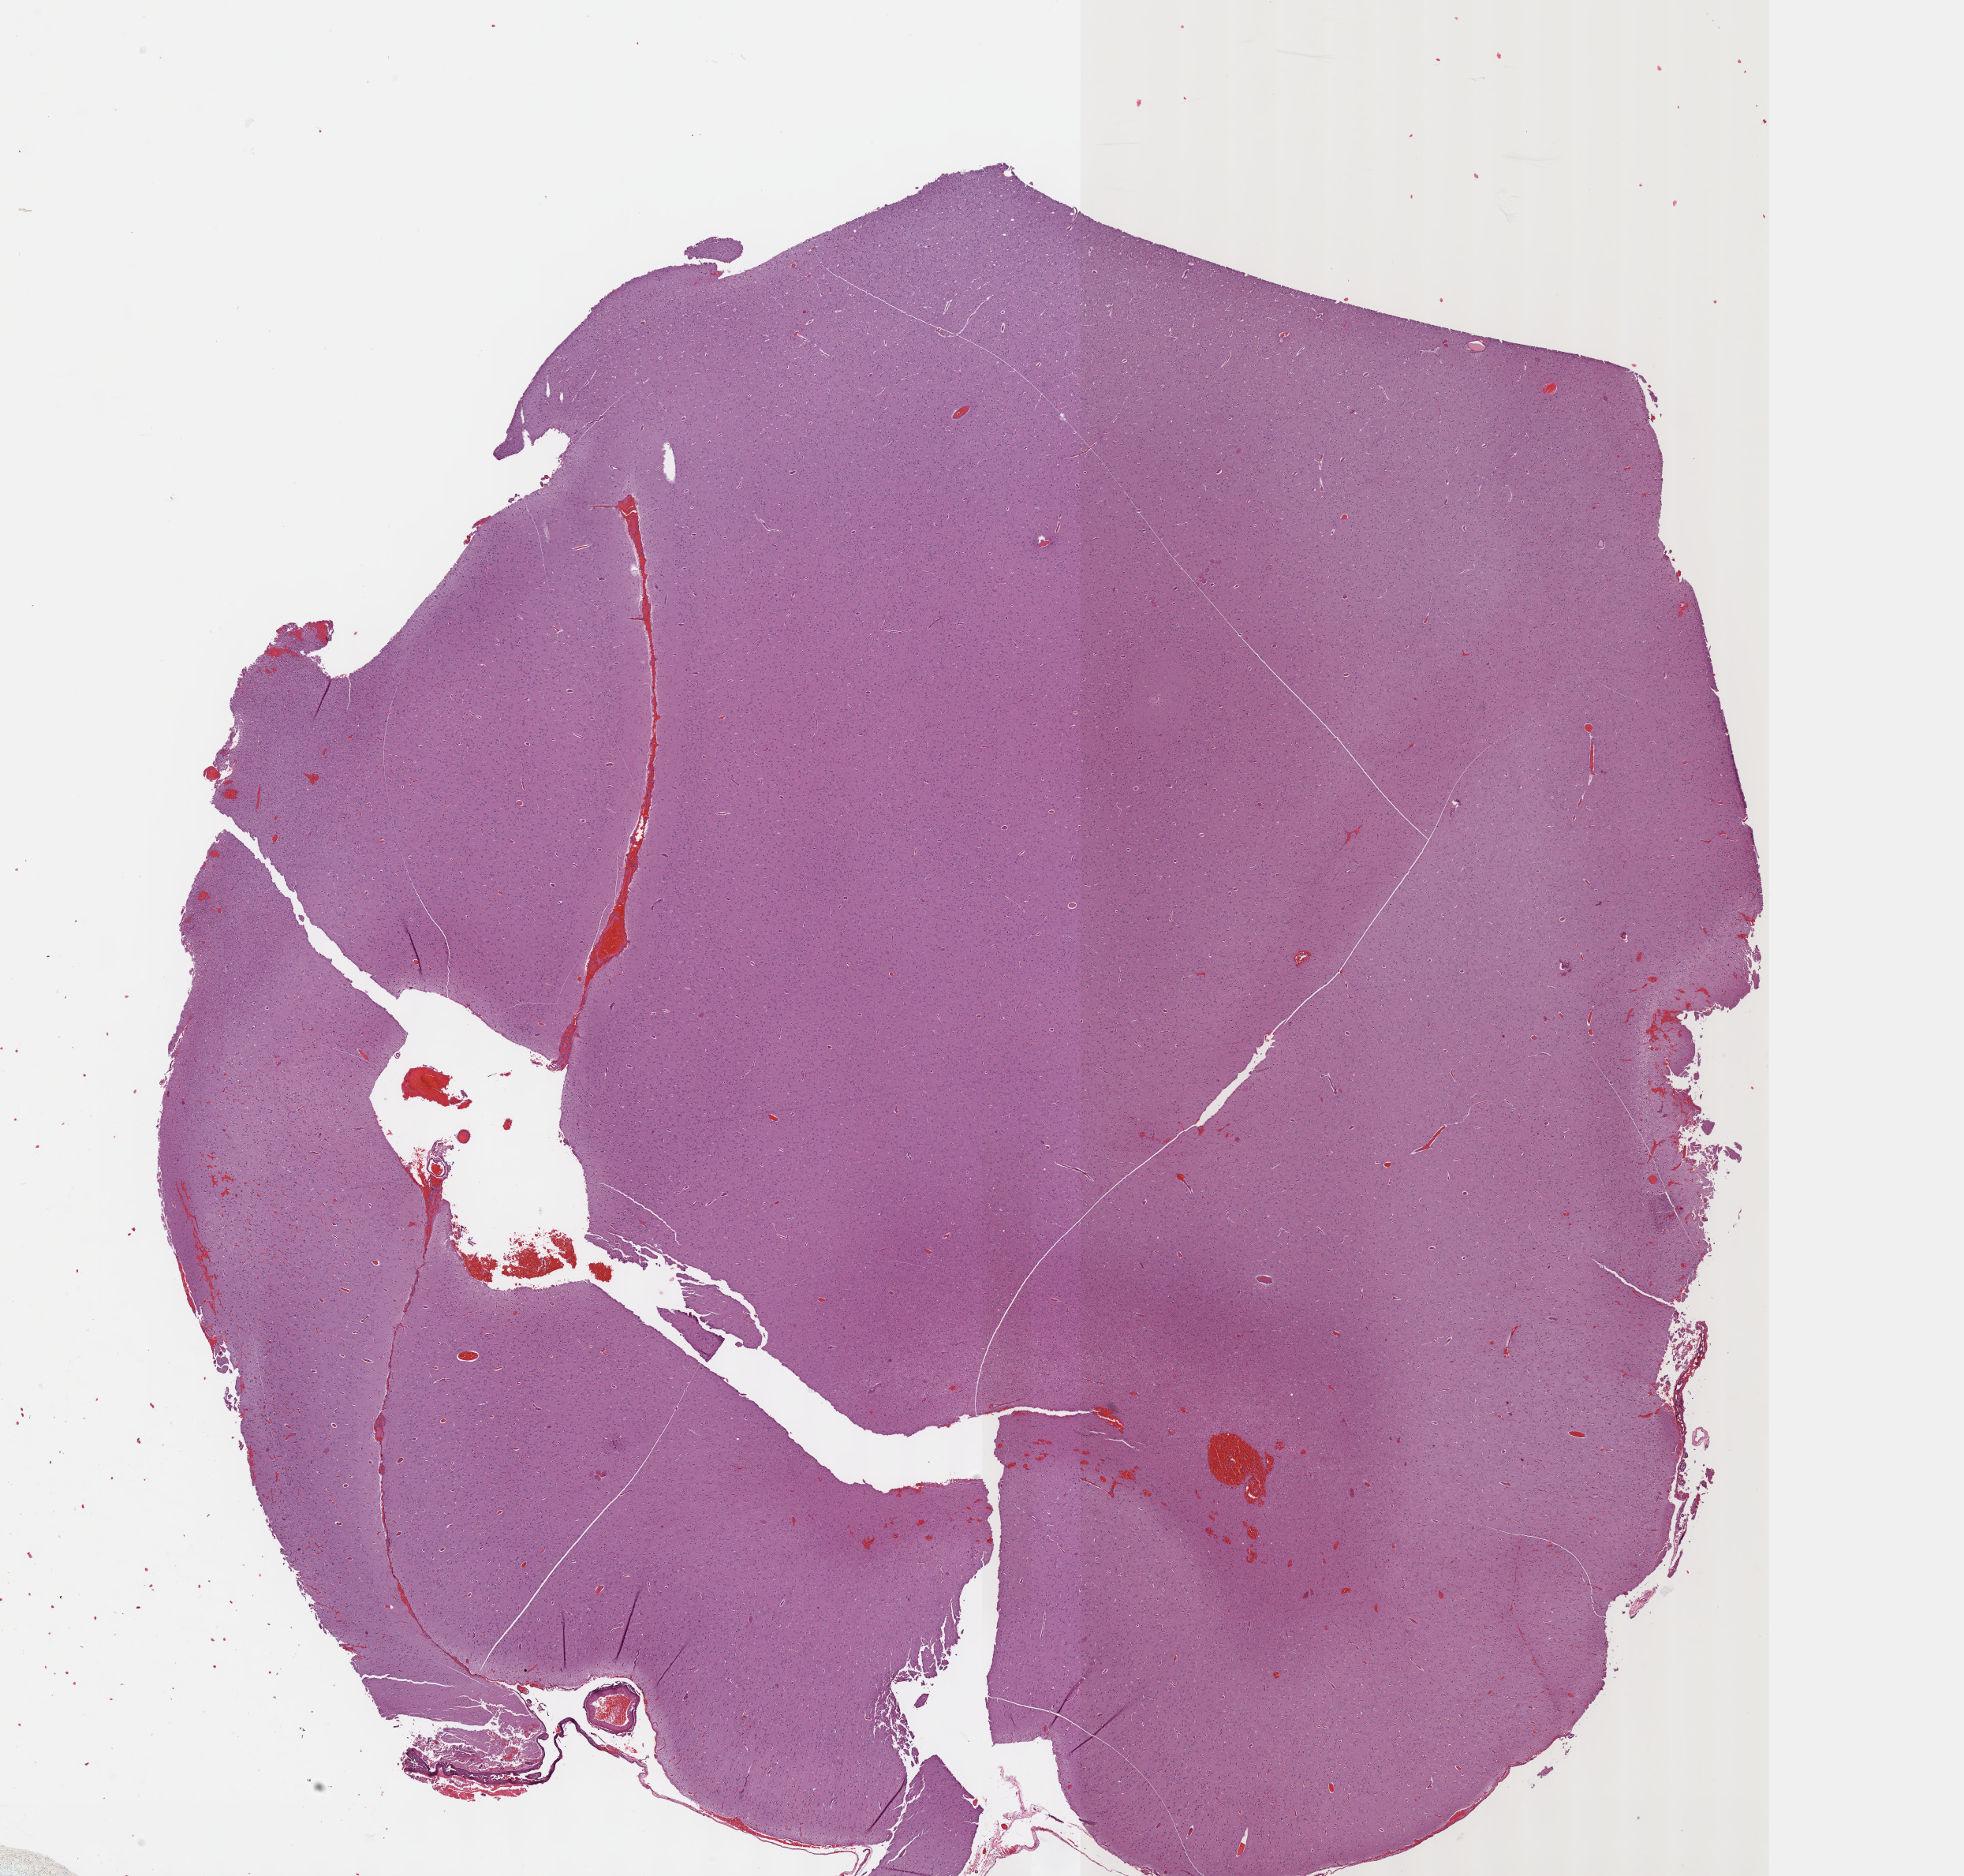
H&E-stained whole-slide image — whole scanned area (about 20.1 x 19.2 mm, slide scanned at 40x) shown as a low-resolution overview. Formalin-fixed paraffin-embedded (FFPE) diagnostic section. Primary tumour sample from the brain. Male, age 35 years at initial diagnosis. Histologic grade: G3 (poorly differentiated).
Diagnosis: Oligodendroglioma, anaplastic (cerebrum). Laterality: left.